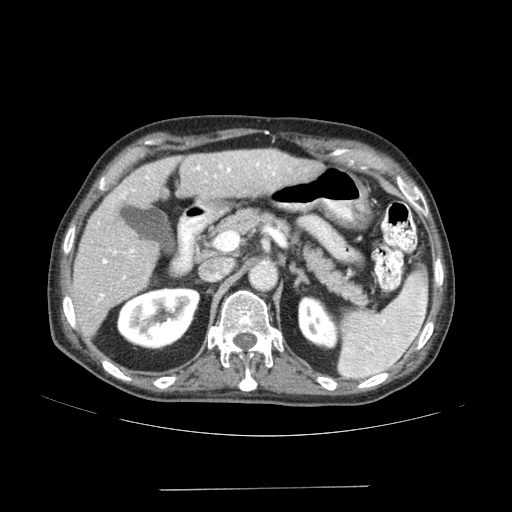
Contrast-enhanced abdominal CT (liver protocol), one axial slice; reconstruction kernel SOFT; soft-tissue window (W 400 / L 40 HU); 512 × 512 image matrix. Case-level facts recorded for this patient, not image findings: diagnosis: hepatocellular carcinoma (patient treated with transarterial chemoembolisation; whether this scan precedes or follows treatment is not stated here); TNM stage (as recorded): Stage-IVA; Child-Pugh class: A; tumour differentiation: poorly differentiated; tumour nodularity: uninodular.
Structures marked on this image (semi-automatic segmentation, software-assisted and operator-edited):
- liver parenchyma outside the tumour (the mass and vessels are separate outlines, so this box may not span the whole liver): bounding box <72,150,322,336> (left, top, right, bottom; pixels)
- liver vessels: <98,162,275,301>